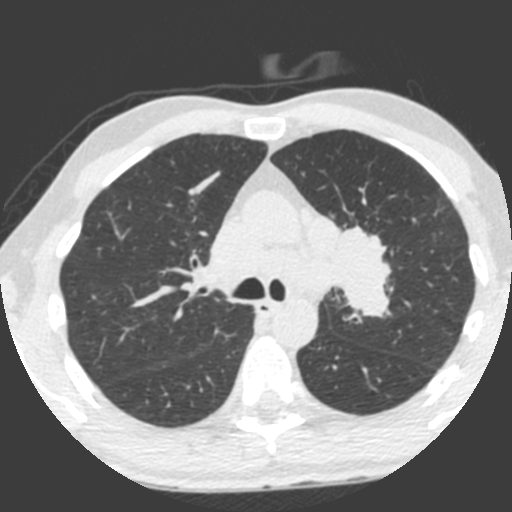
Low-dose screening chest CT, one axial slice; slice 145 of 212 in the series (ordered by position); 120 kVp; lung window (W 1500 / L -600 HU); 2 mm slice thickness; 512 × 512 image matrix, field of view 315 × 315 mm.
Outlined on this slice (manually delineated by an expert):
- lesion 1 (tumor, upper lobe of left lung): box from (x=331, y=225) to (x=392, y=318) px